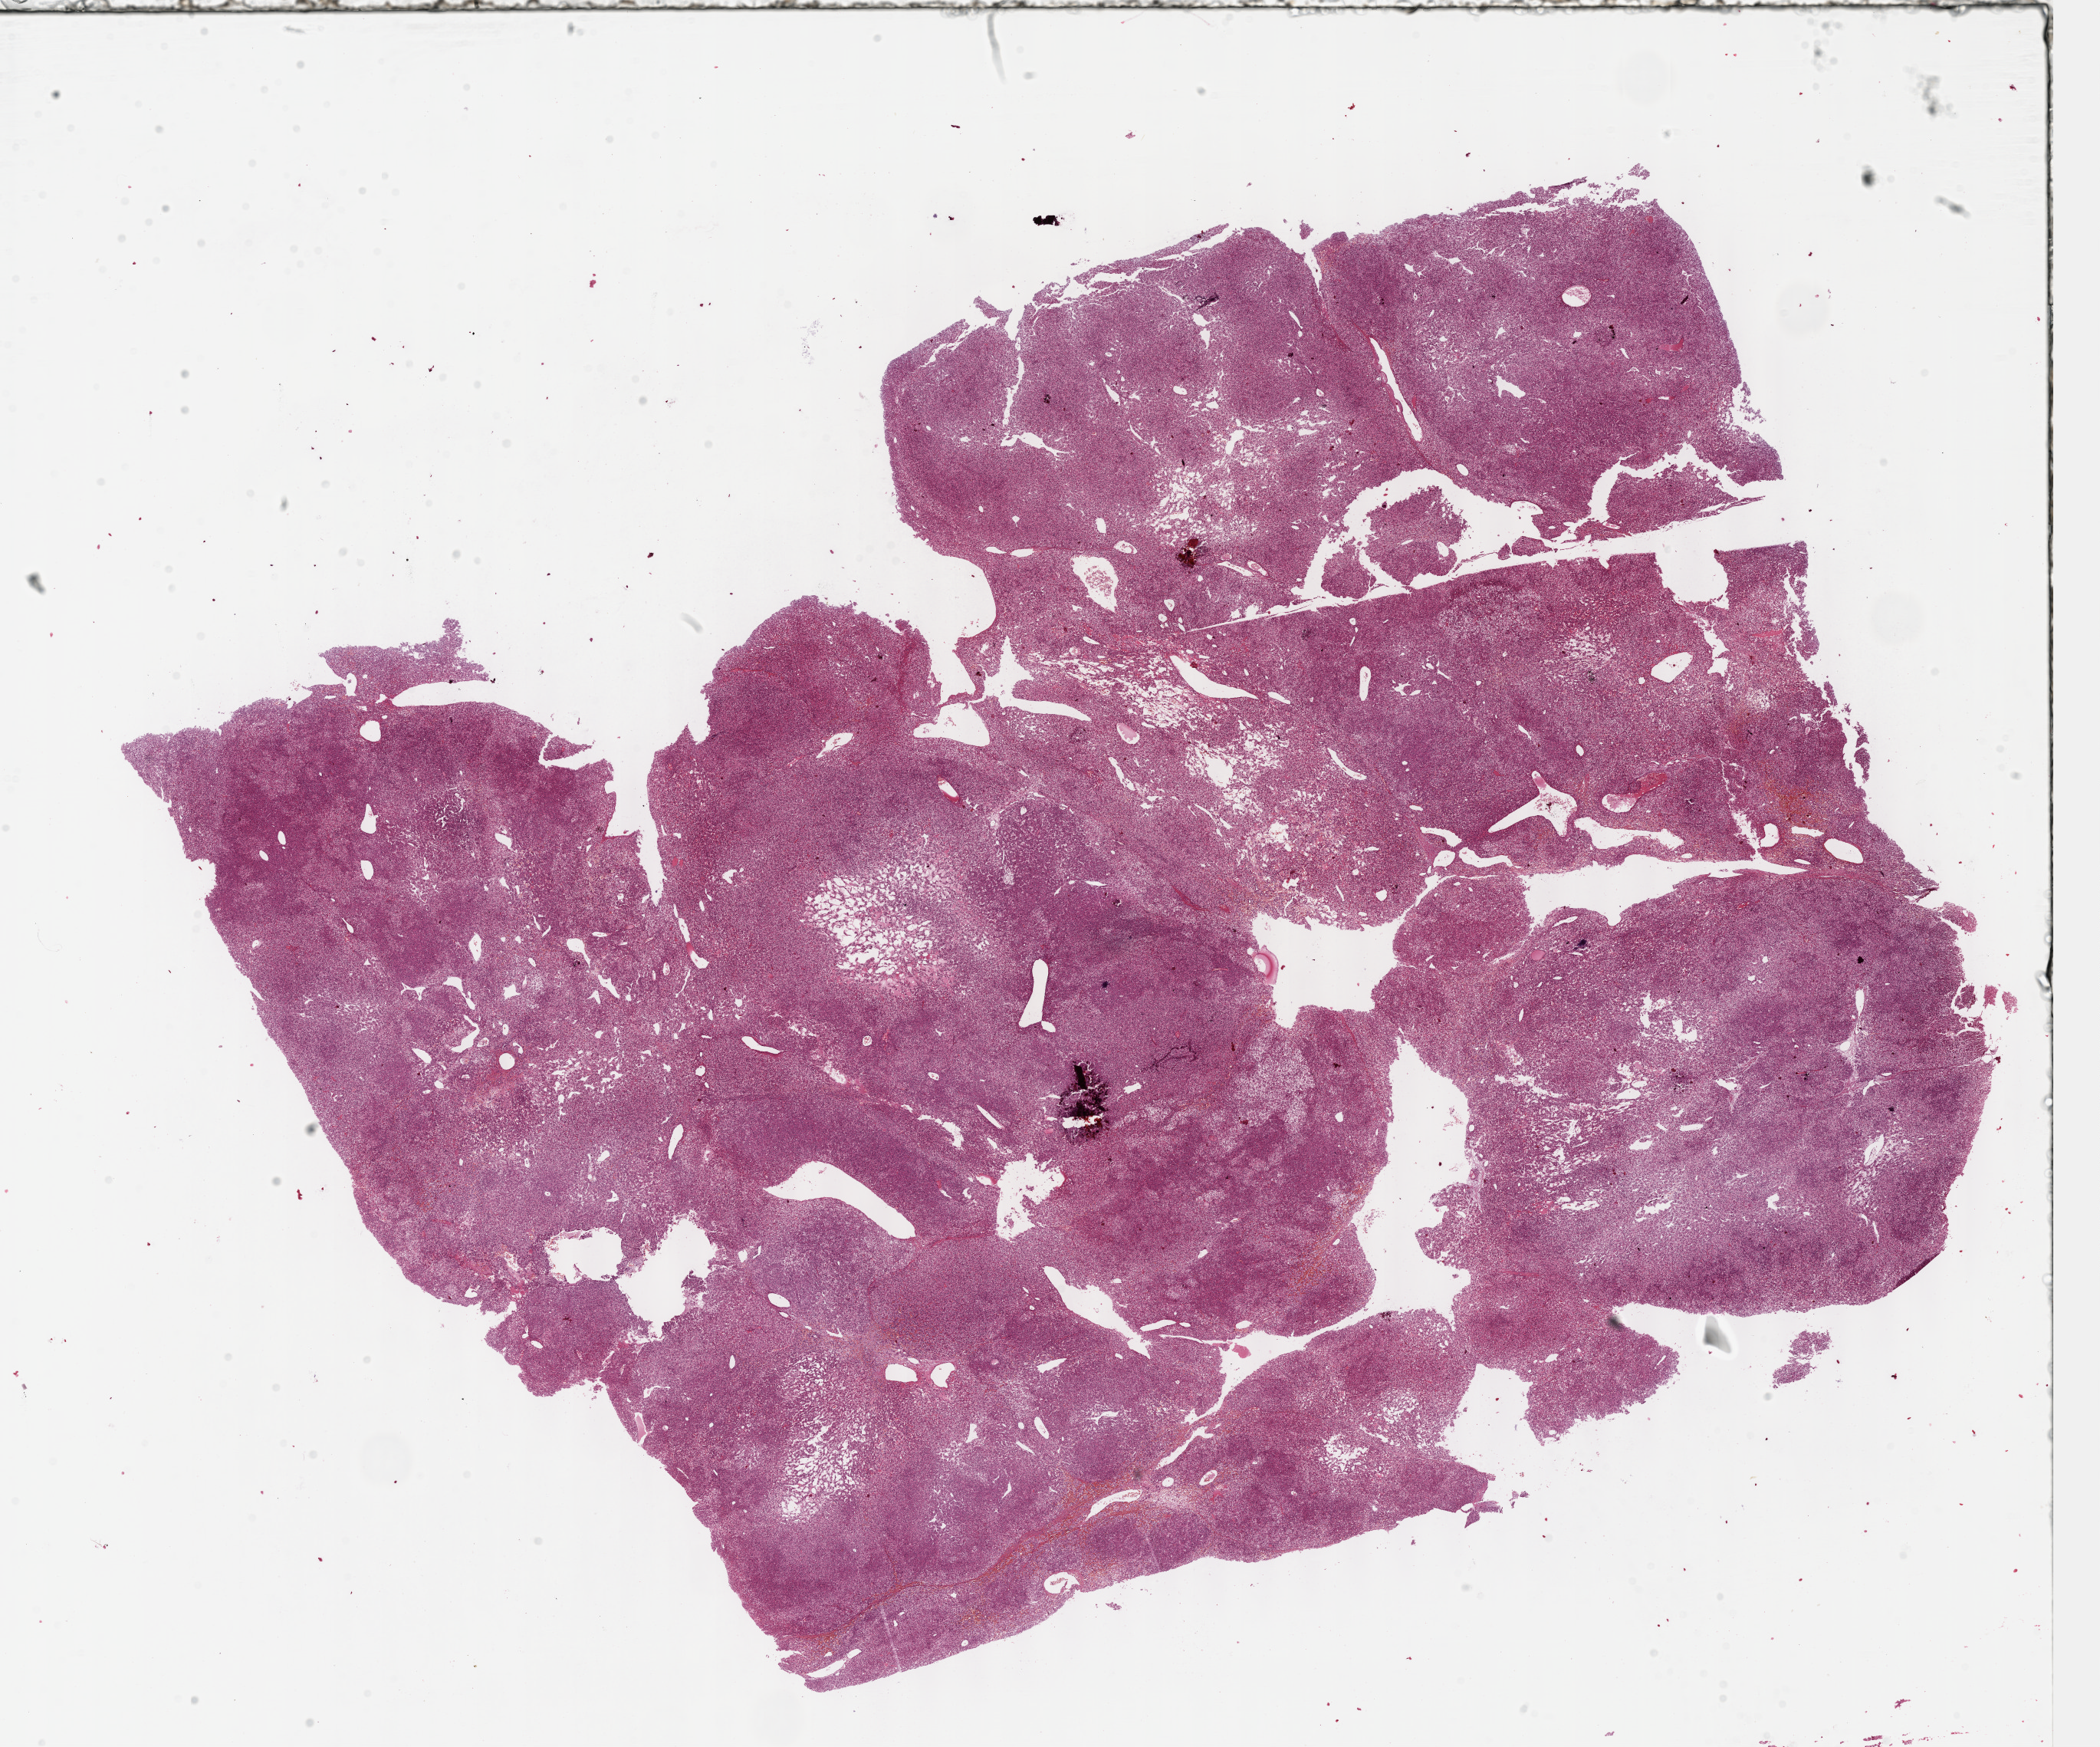
Digitized Hematoxylin and eosin (H&E) stained tissue section (whole slide) — whole scanned area (about 22.1 x 18.4 mm, acquisition: 40x scan) shown as a low-resolution overview. FFPE section. Sample: primary tumour, liver. Patient: male, age at initial diagnosis 58 years. Histologic grade: G1 (well differentiated).
Histologic diagnosis: Hepatocellular carcinoma, NOS. AJCC pathologic stage: IIIA (6th edition).